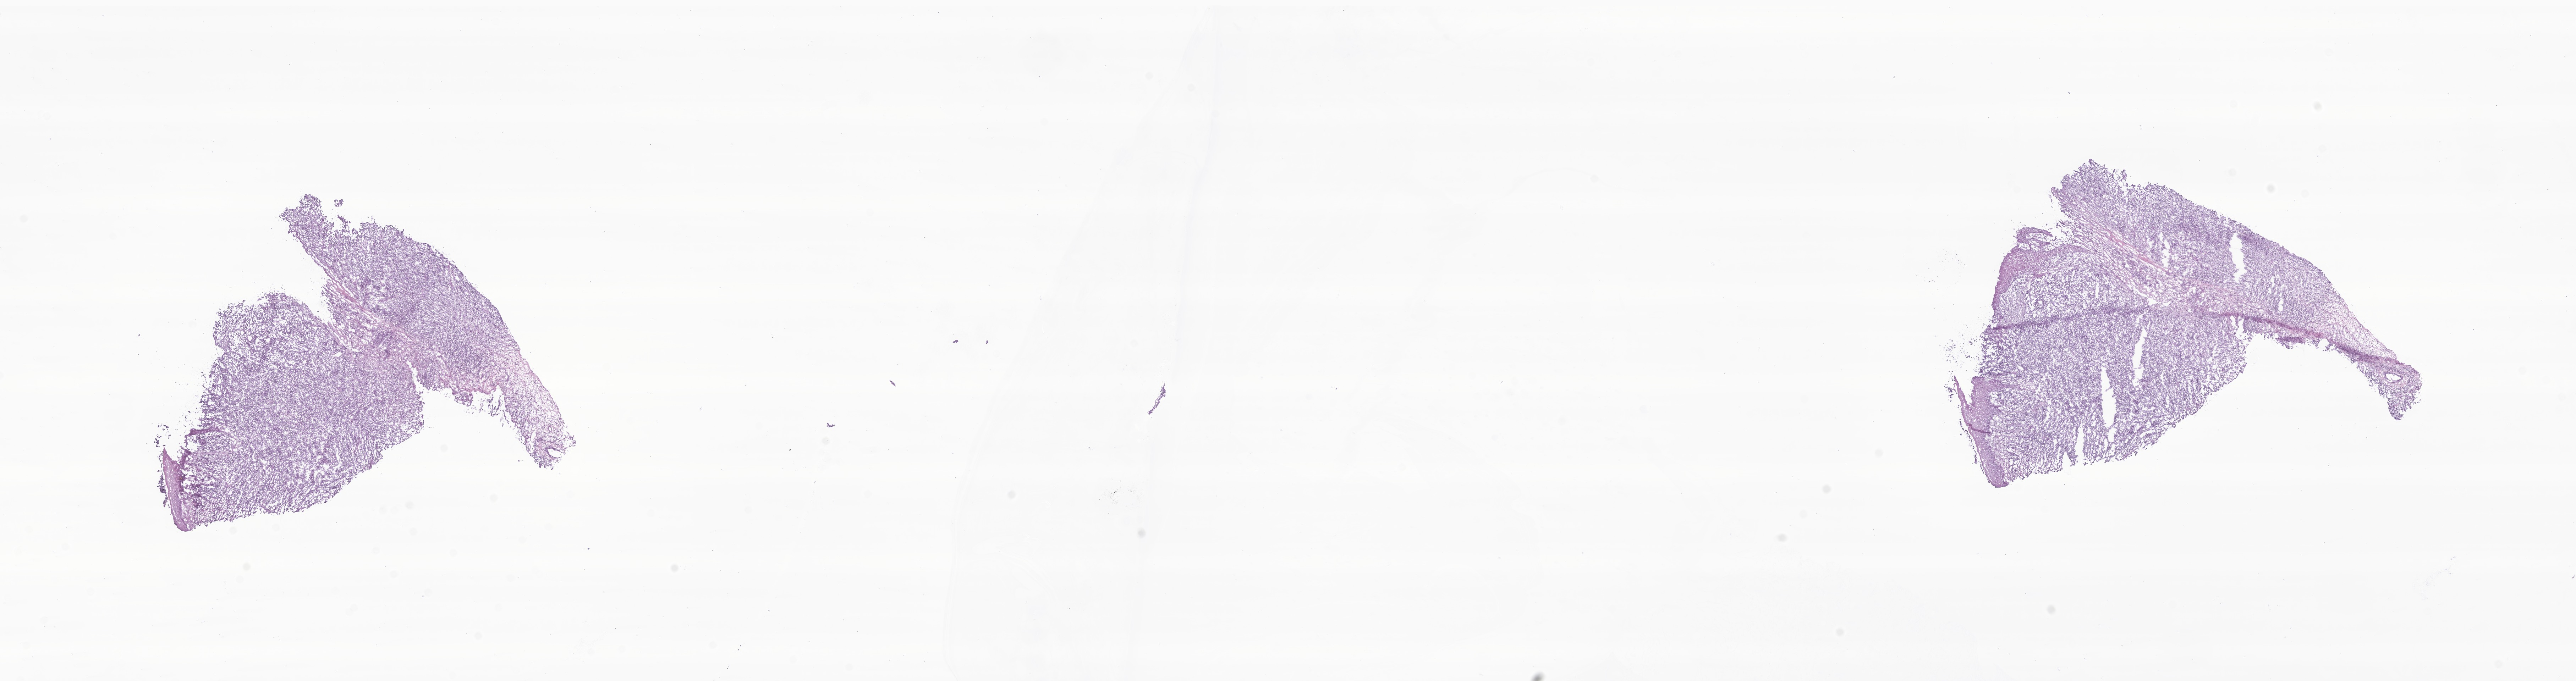
Digitized haematoxylin and eosin-stained section of tumor tissue from the oropharynx — shown as a low-resolution overview of the whole scanned area (about 30.6 x 8.1 mm); cryosection (OCT / tissue freezing medium). Female patient, age 182 months (15 years 2 months).
• diagnosis (ICD-O-3 morphology term): Embryonal rhabdomyosarcoma, NOS